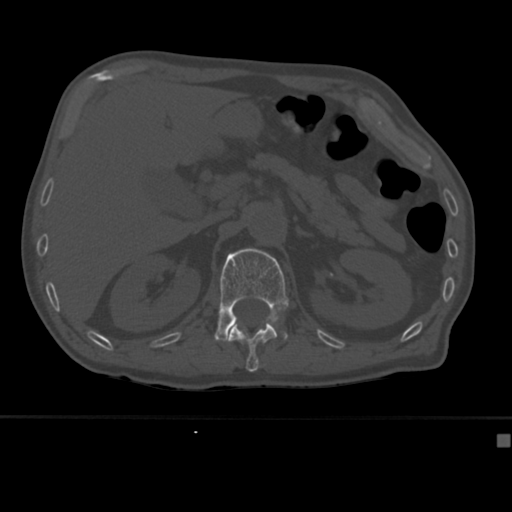
CT including the spine, one axial slice; position 177 of 430 along the scan axis; reconstruction kernel Br40s; bone window (W 1800 / L 400 HU); 1.5 mm slice thickness; 512 × 512 image matrix, field of view 337 × 337 mm. Patient: male, 64 years. Case-level facts recorded for this patient, not image findings: primary cancer: uterus.
Outlined on this slice (semi-automatic segmentation, software-assisted and operator-edited):
- L1 vertebra: bounding box [x1, y1, x2, y2] px = [214, 248, 289, 342]
- T12 vertebra: [229, 319, 278, 372]